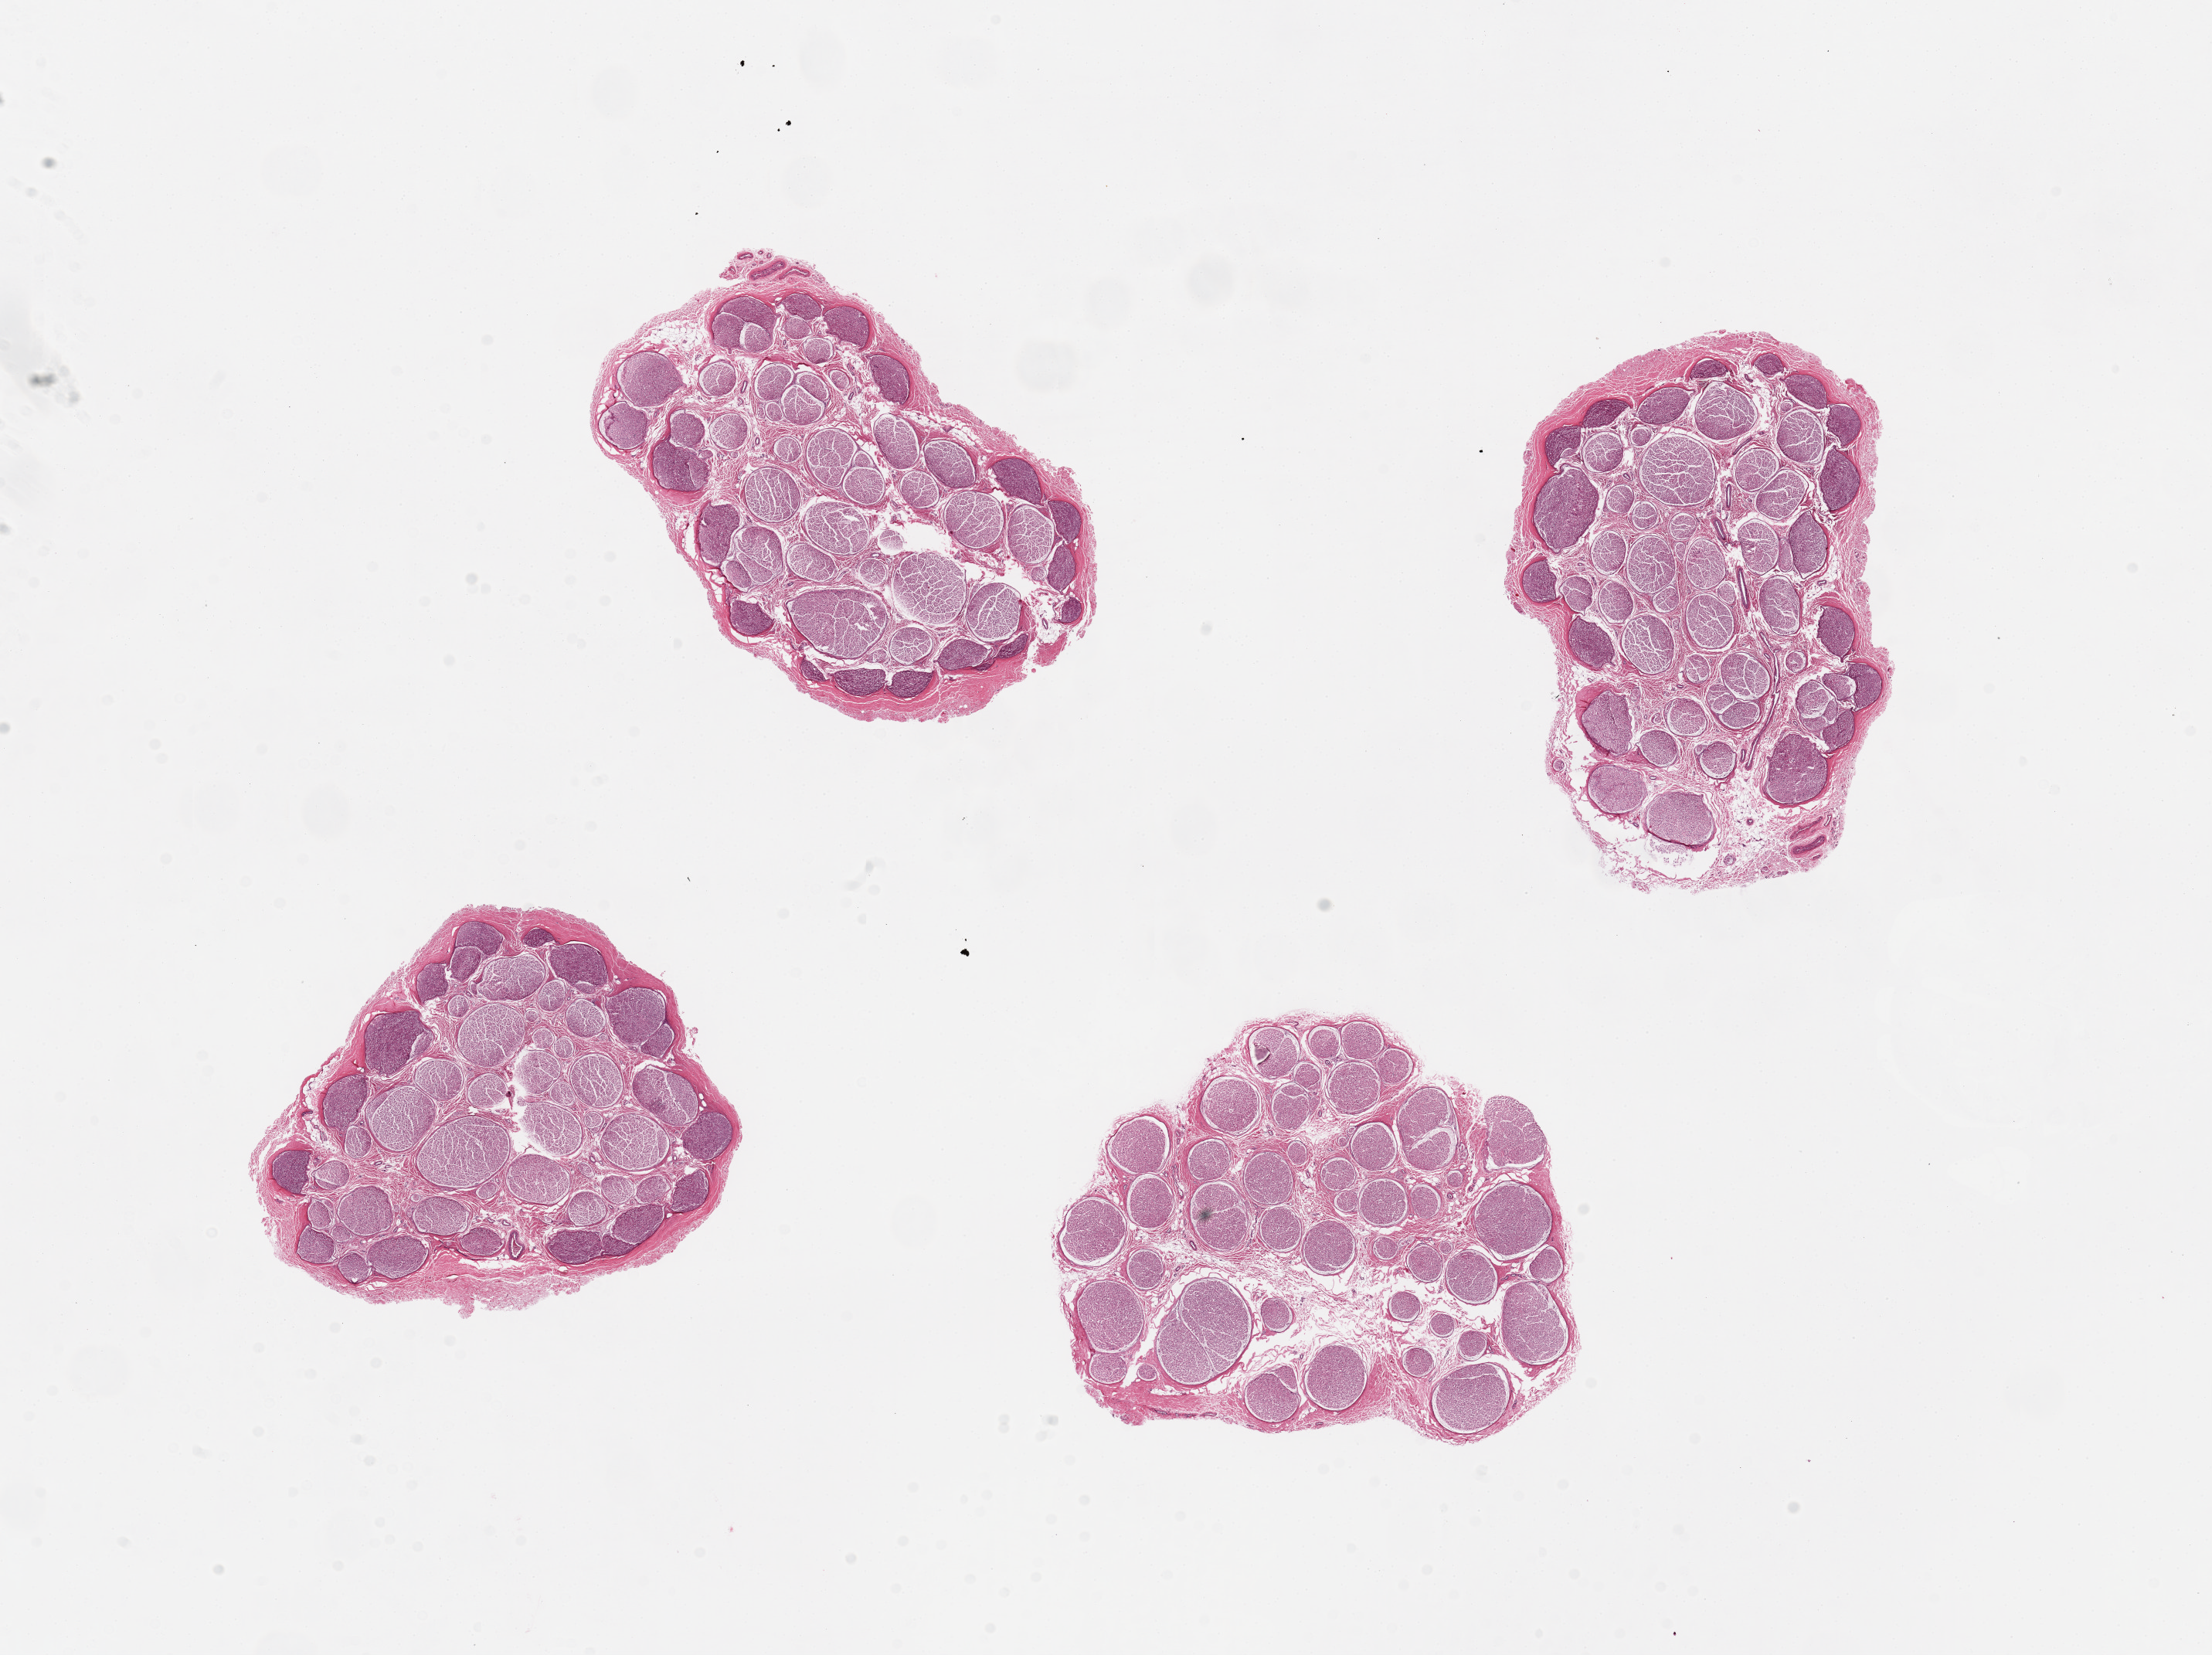
Digitized hematoxylin and eosin (H&E)-stained section, whole scanned area (about 22.6 x 16.9 mm) shown as a low-resolution overview; PAXgene-fixed, paraffin-embedded tissue; section of tibial nerve (target tissue); tissue donor sample. Female donor.
- pathologist's review note for this sample: 4 pieces. up to 6x4mm; Well dissected